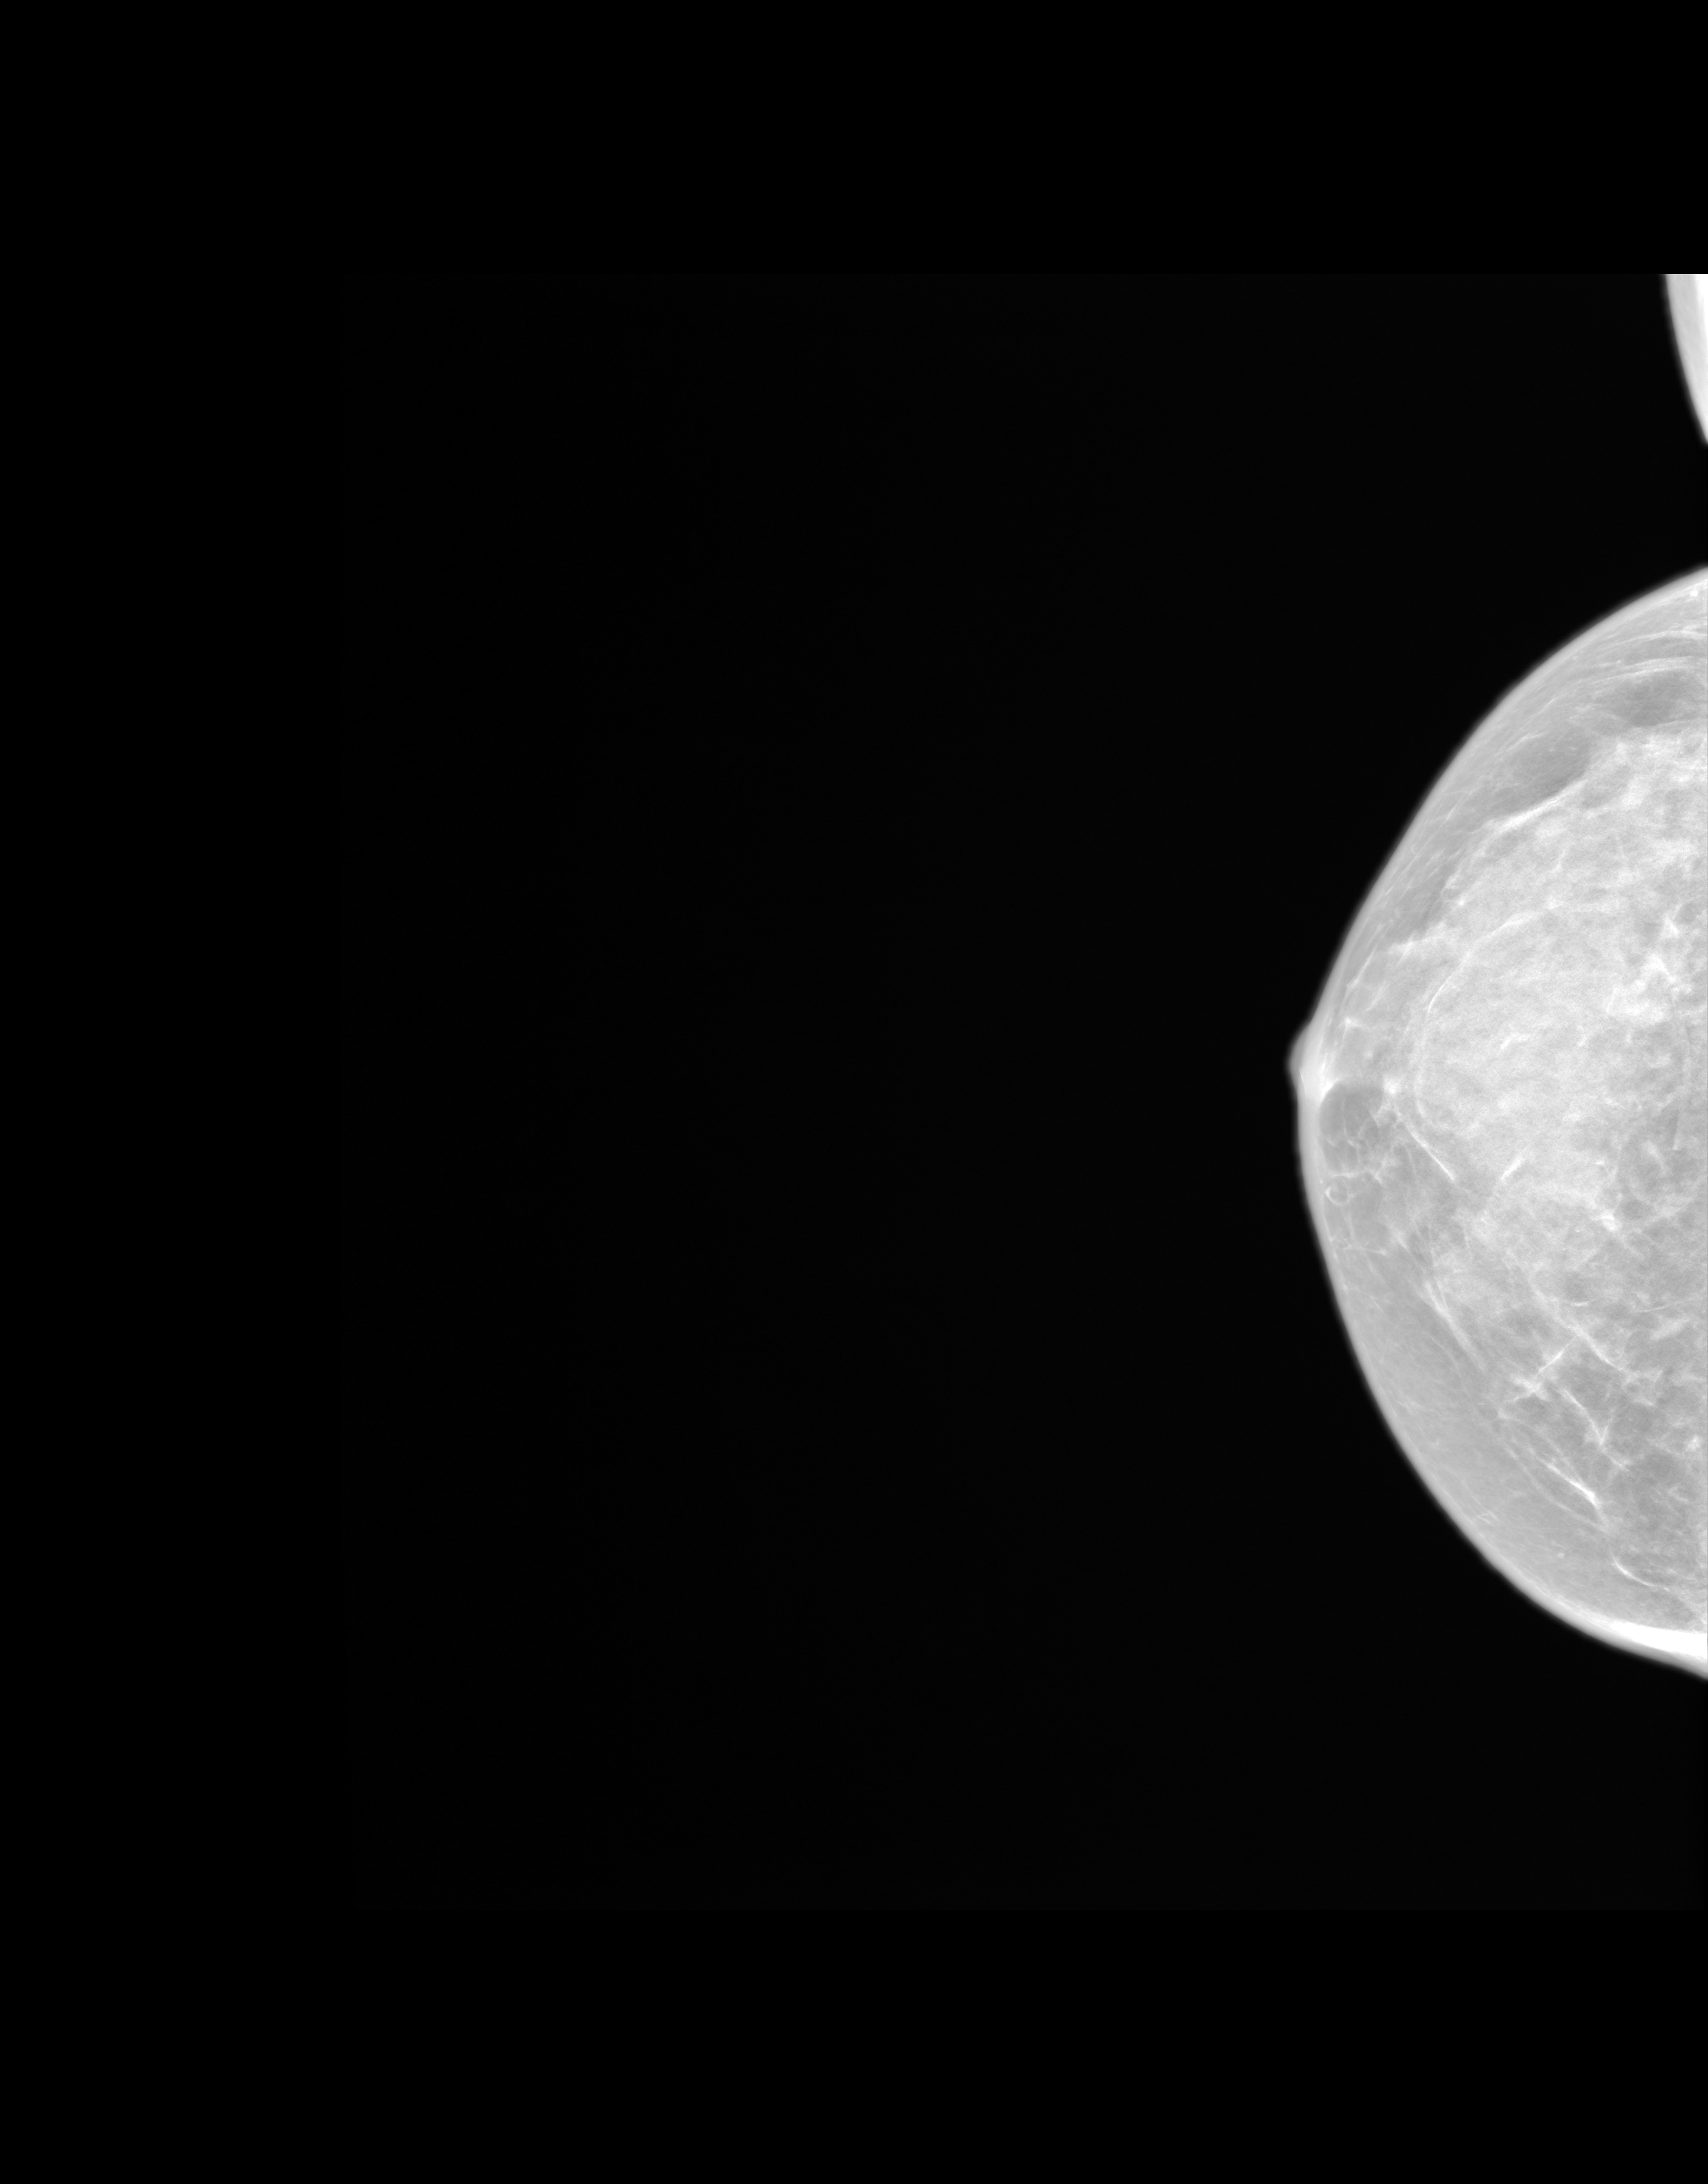
Synthesized 2-D mammogram reconstructed from digital breast tomosynthesis, right breast, craniocaudal (CC) view, screening examination. Patient: female, 55 years.
Breast density at the screening exam (both breasts): extremely dense (BI-RADS density category d). Final BI-RADS category for the screening round (tomosynthesis exam, both breasts): category 1. Recall: no recall after this screen.